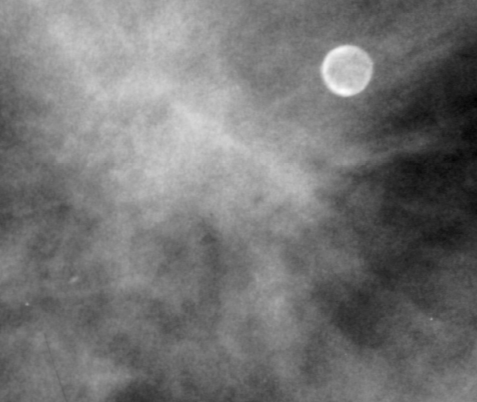
Crop from a digitized film mammogram around one marked abnormality, right breast, CC view.
Marked abnormality: mass, shape irregular, margins spiculated; BI-RADS assessment category 5; subtlety rating 3 on a 1 (subtle) to 5 (obvious) scale; pathology (as recorded): benign.